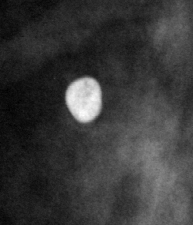
Region of interest cut from a scanned film mammogram (one marked finding), right breast, MLO view, BI-RADS breast density category 2 (scale 1–4).
Finding: calcifications, morphology lucent center; BI-RADS assessment category 2; benign; no additional work-up was recommended (benign without callback).